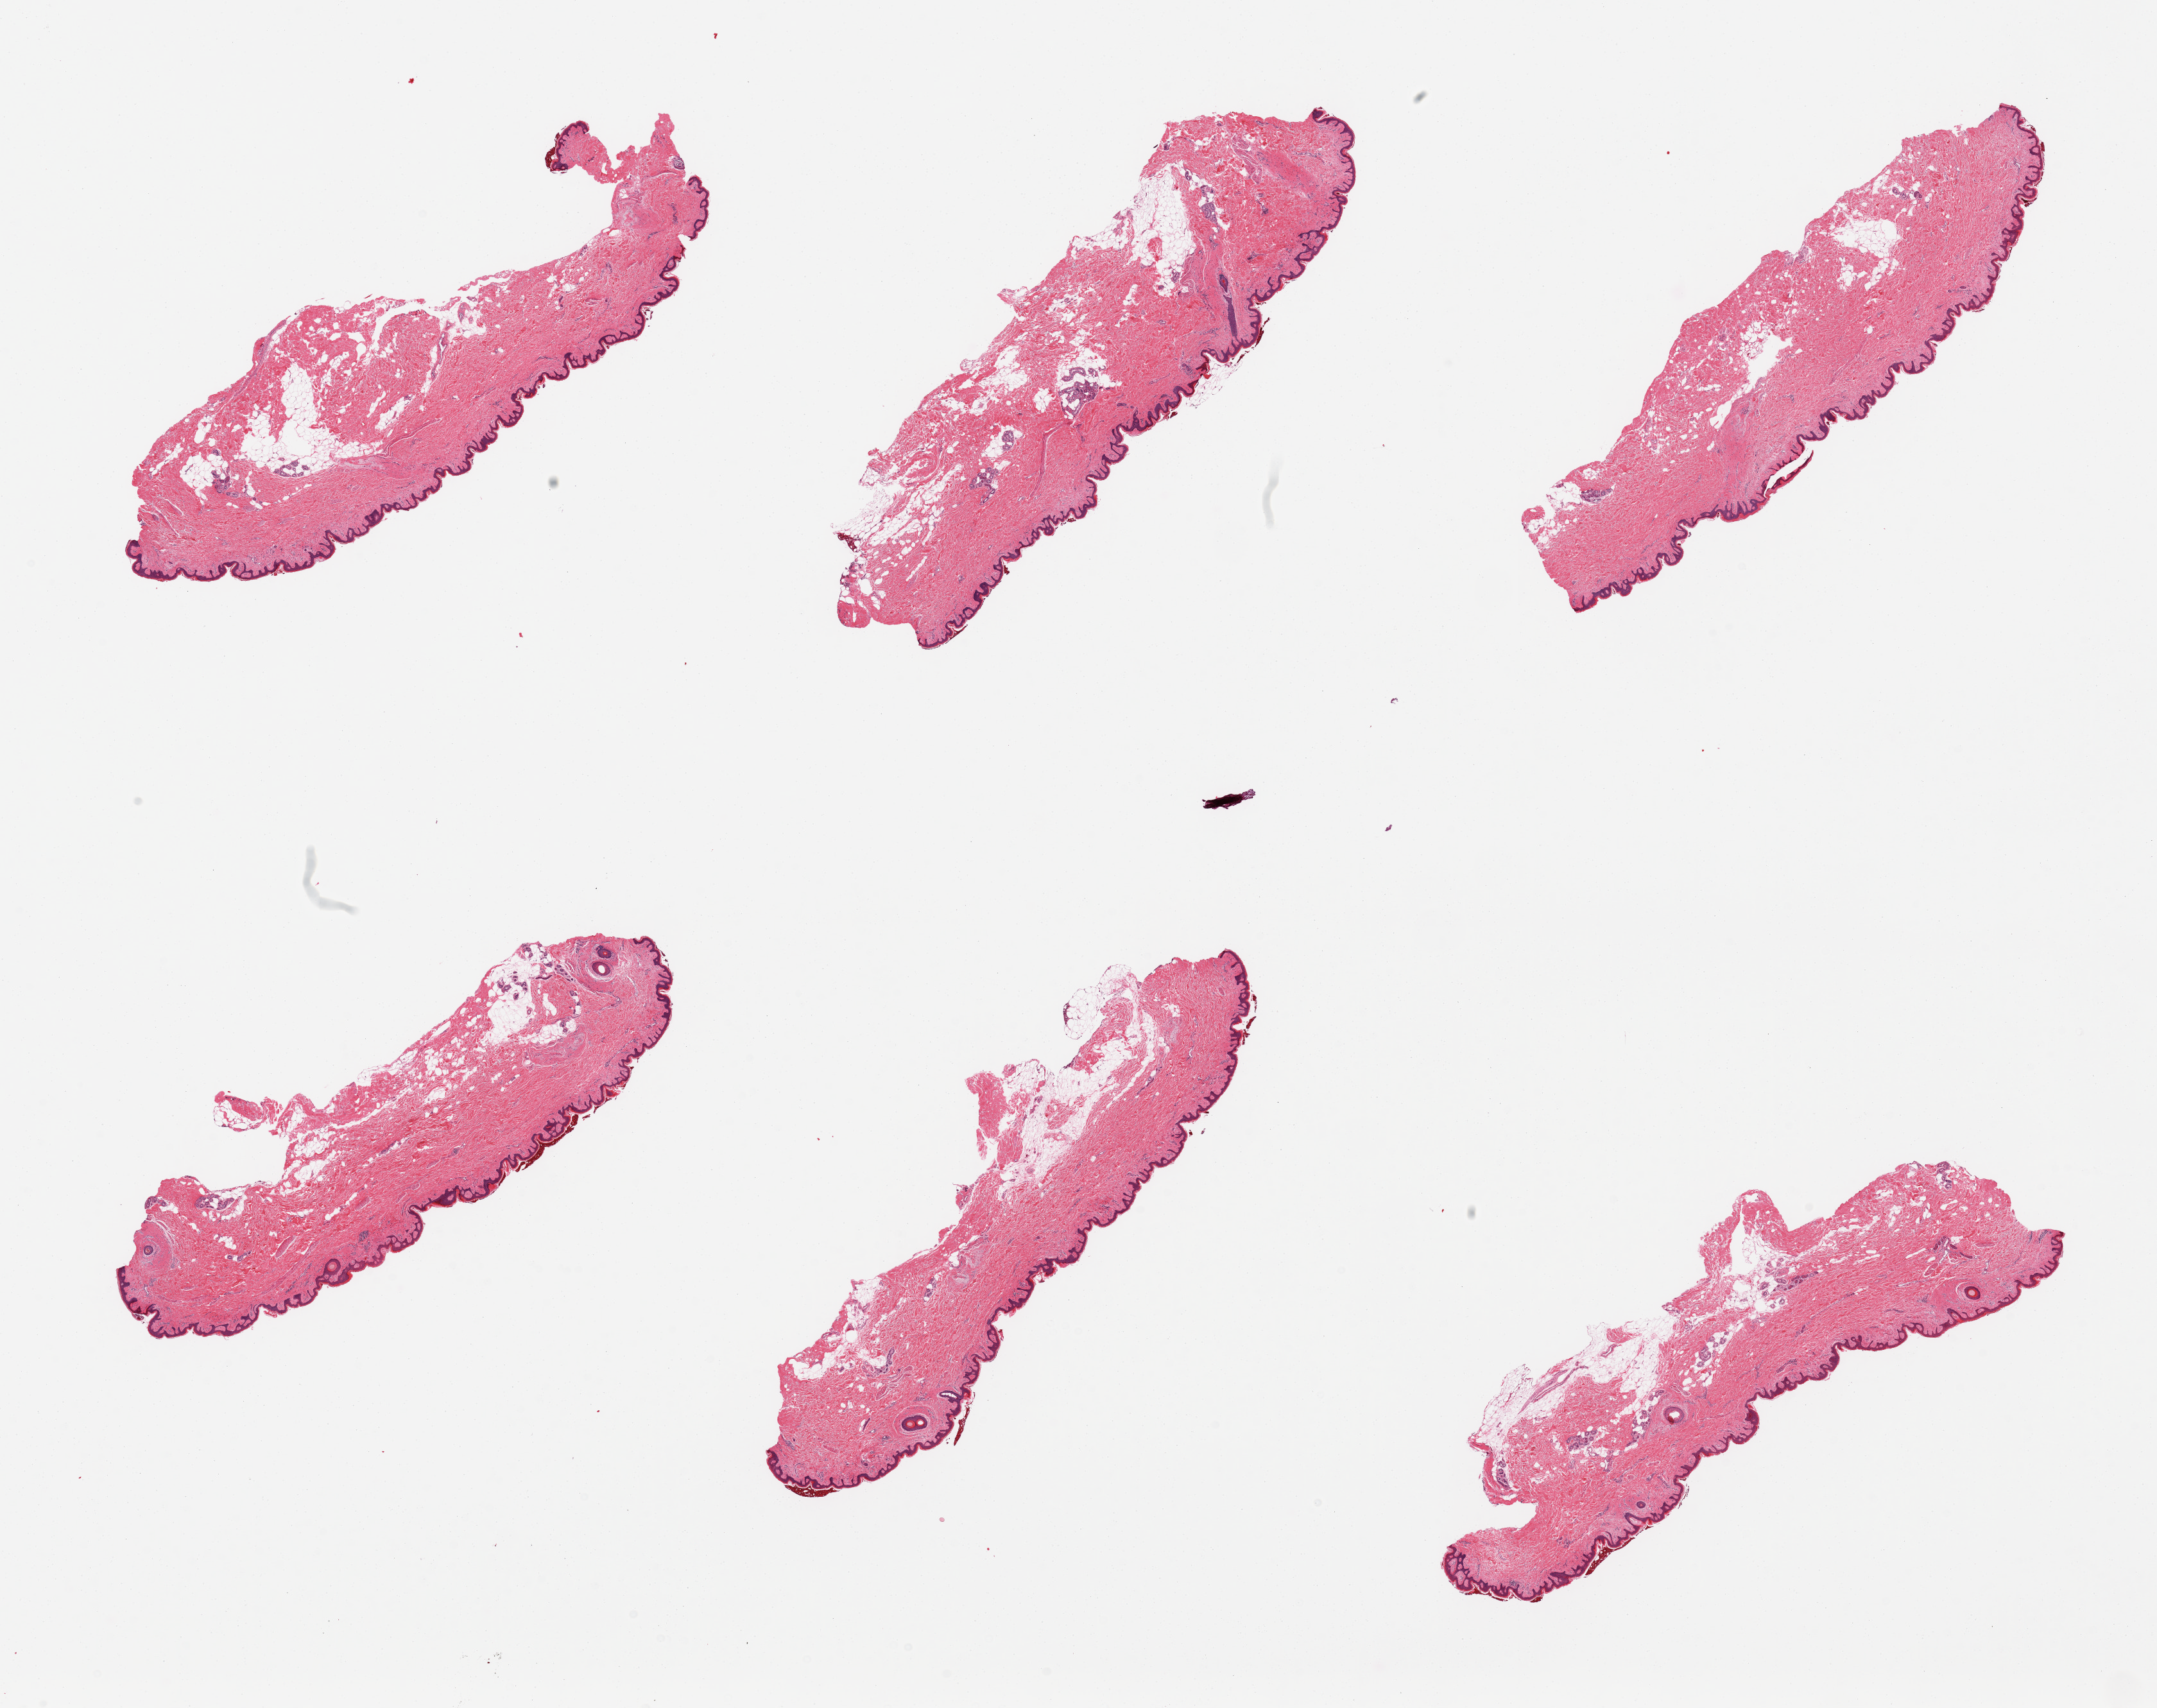
Hematoxylin and eosin (H&E) whole-slide image, whole scanned area (about 26.6 x 21.0 mm, slide scanned at 20x) shown as a low-resolution overview; PAXgene-fixed paraffin-embedded (PFPE) section; target tissue: skin of suprapubic region; donor tissue sample. Male donor.
Reviewer comment on this tissue sample: 6 pieces, 5-10% attached and internal fat, overlying crust of degenerating cells.